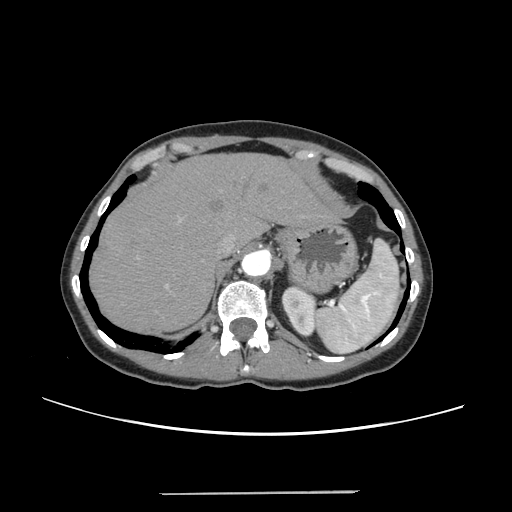
Contrast-enhanced abdominal CT, one axial slice; slice 192 of 240 in the series (ordered by position); 120 kVp; intravenous contrast given; soft-tissue window (W 400 / L 40 HU); 1.25 mm slice thickness; 512 × 512 image matrix. Female patient, age 60 years. From the clinical record (not read from this slice): diagnosis: colorectal cancer liver metastases, imaged before liver resection; multiple liver metastases: no; largest metastasis: 1.5 cm; chemotherapy before resection: yes.
Outlined on this slice (outlined manually by an expert reader):
- hepatic veins: bounding box (x1, y1, x2, y2) in pixels: (217, 237, 234, 254)
- liver: (90, 155, 331, 333)
- planned liver remnant (the part of the liver to remain after resection): (90, 155, 331, 333)
- portal vein (with intrahepatic branches): (165, 217, 182, 288)